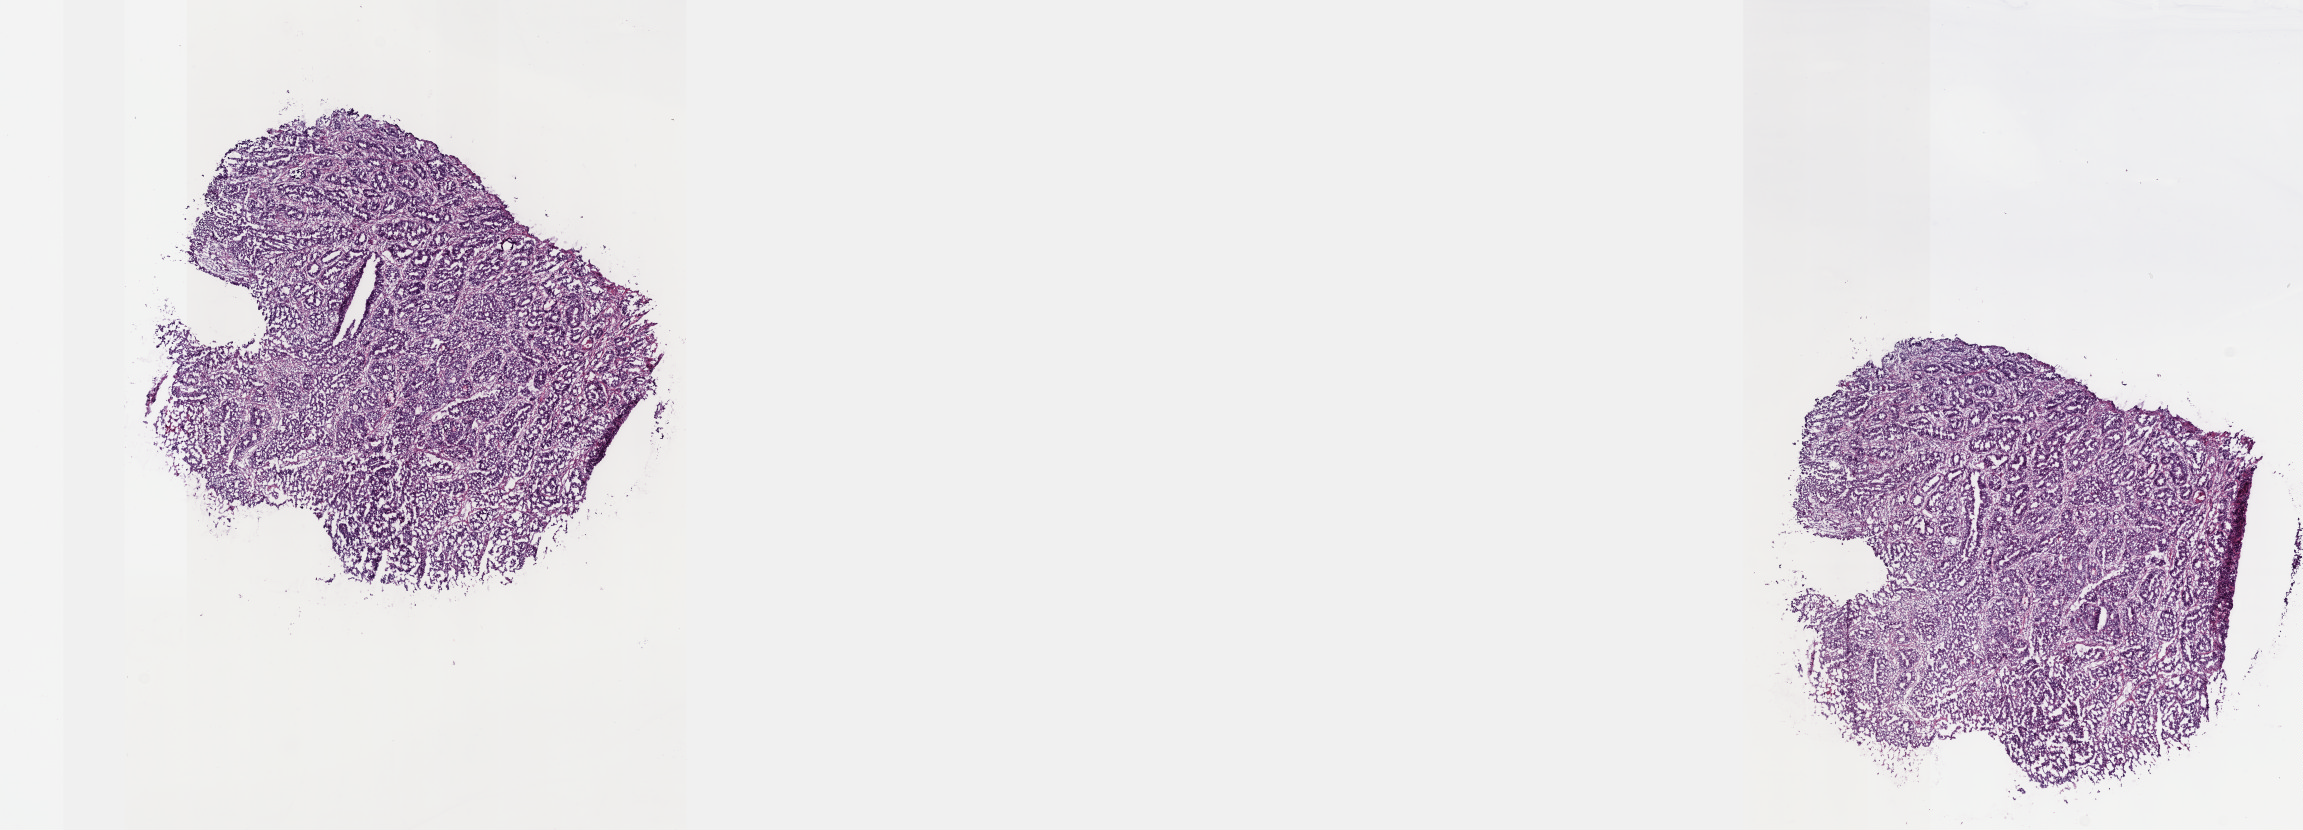
Digitized Hematoxylin and eosin (H&E) stained tissue section (whole slide), a low-resolution overview of the entire scanned area, about 18.6 x 6.7 mm (acquisition: 40x scan). Frozen section from the top of the tissue portion. Primary tumour sample from the stomach. Patient: male, age at initial diagnosis 48 years.
Histologic diagnosis: Adenocarcinoma, intestinal type (cardia, NOS).